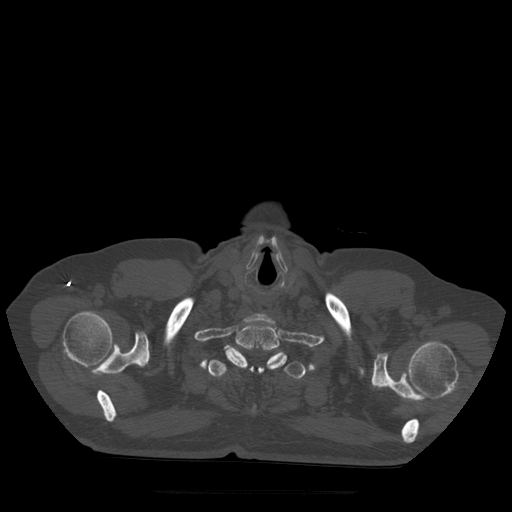
CT including the spine, one axial slice. Slice 436 of 522 in the series (ordered by position). Bone window (W 1800 / L 400 HU). 1.25 mm slice thickness. 512 × 512 image matrix. Patient age 72 years. From the clinical record (not read from this slice): primary cancer: prostate.
Outlined on this slice (semi-automatically segmented with operator editing):
- T1 vertebra: bounding box <224,321,288,370> (left, top, right, bottom; pixels)
- T2 vertebra: <208,345,306,411>